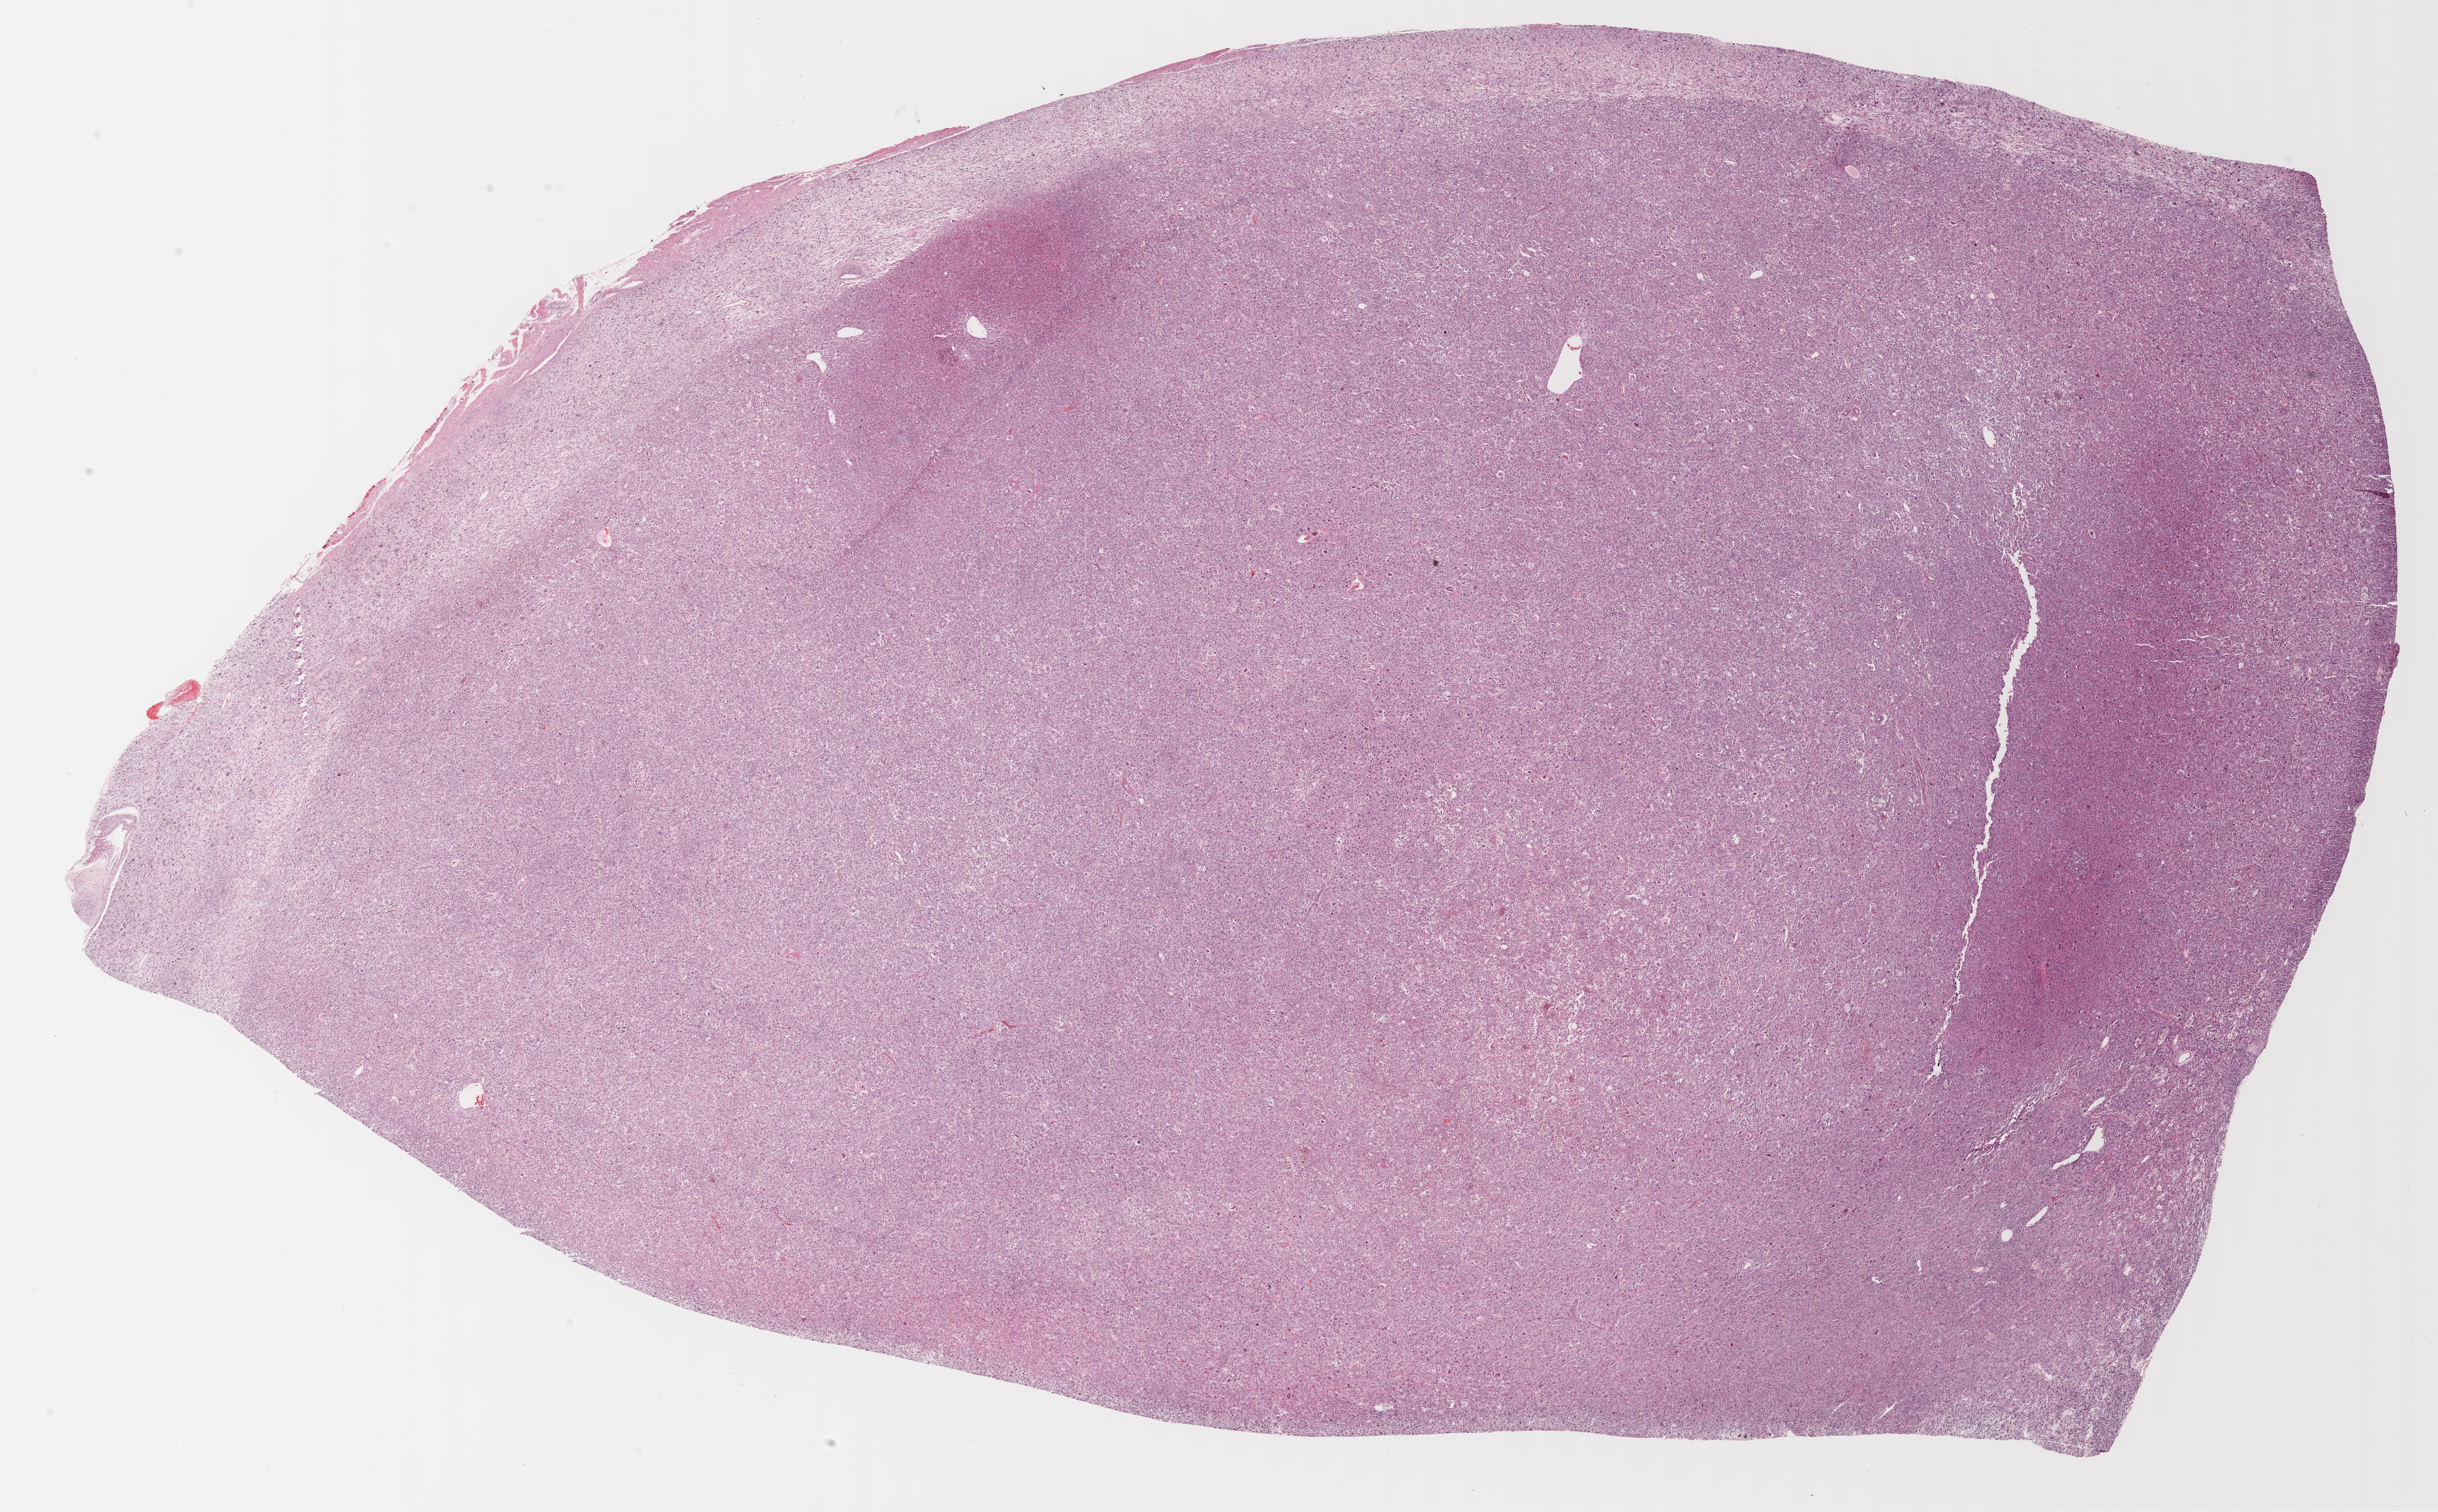
H&E whole-slide image — whole scanned area (about 30.2 x 18.7 mm) shown as a low-resolution overview; formalin-fixed paraffin-embedded (FFPE) diagnostic section; primary tumour sample from the connective, subcutaneous and other soft tissues. Patient: female, age at initial diagnosis 61 years.
• pathologic diagnosis: Undifferentiated sarcoma (connective, subcutaneous and other soft tissues of lower limb and hip)